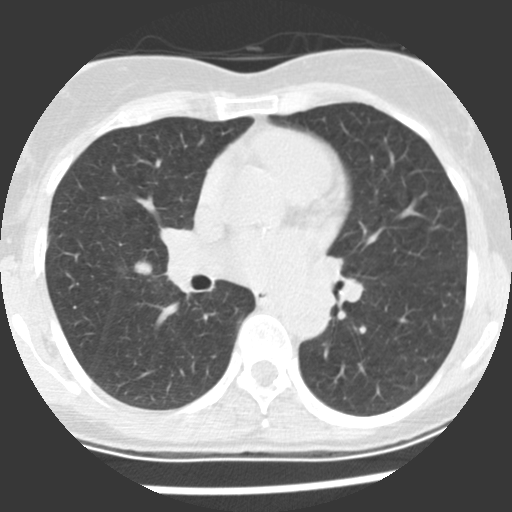
Low-dose screening chest CT, axial slice, first (baseline) screen, lung window (W 1500 / L -600 HU), 2.5 mm slice thickness, standard (soft-tissue) reconstruction kernel (STANDARD), slice 109 of 225 in the series, 512 × 512 image matrix, field of view 270 × 270 mm. Female participant, aged 60 years at enrolment. Current smoker at enrolment.
Expert-annotated lung lesion, bounding box (x1, y1, x2, y2) in pixels: (115, 249, 175, 294). The screening reader recorded 2 non-calcified nodules or masses ≥4 mm on this exam; which of them this box marks is not recorded. Lung cancer was diagnosed 10 days after this screen: adenocarcinoma, NOS, right upper lobe, stage IIIA (AJCC 6th edition), 20 mm at pathology.